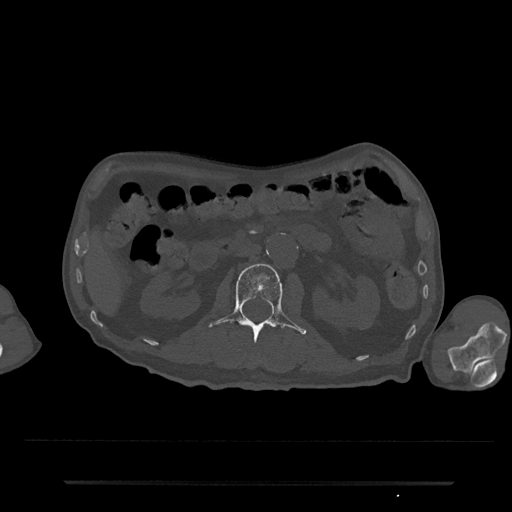
CT including the spine, one axial slice. Slice 67 of 797 in the series (ordered by position). Reconstruction kernel Br40s/3. 120 kVp. Bone window (W 1800 / L 400 HU). 0.5 mm slice thickness. 512 × 512 image matrix. Patient: male, 74 years. From the clinical record (not read from this slice): primary cancer: prostate.
Outlined on this slice (semi-automatic segmentation, software-assisted and operator-edited):
- L2 vertebra: bounding box [x1, y1, x2, y2] px = [208, 263, 306, 342]